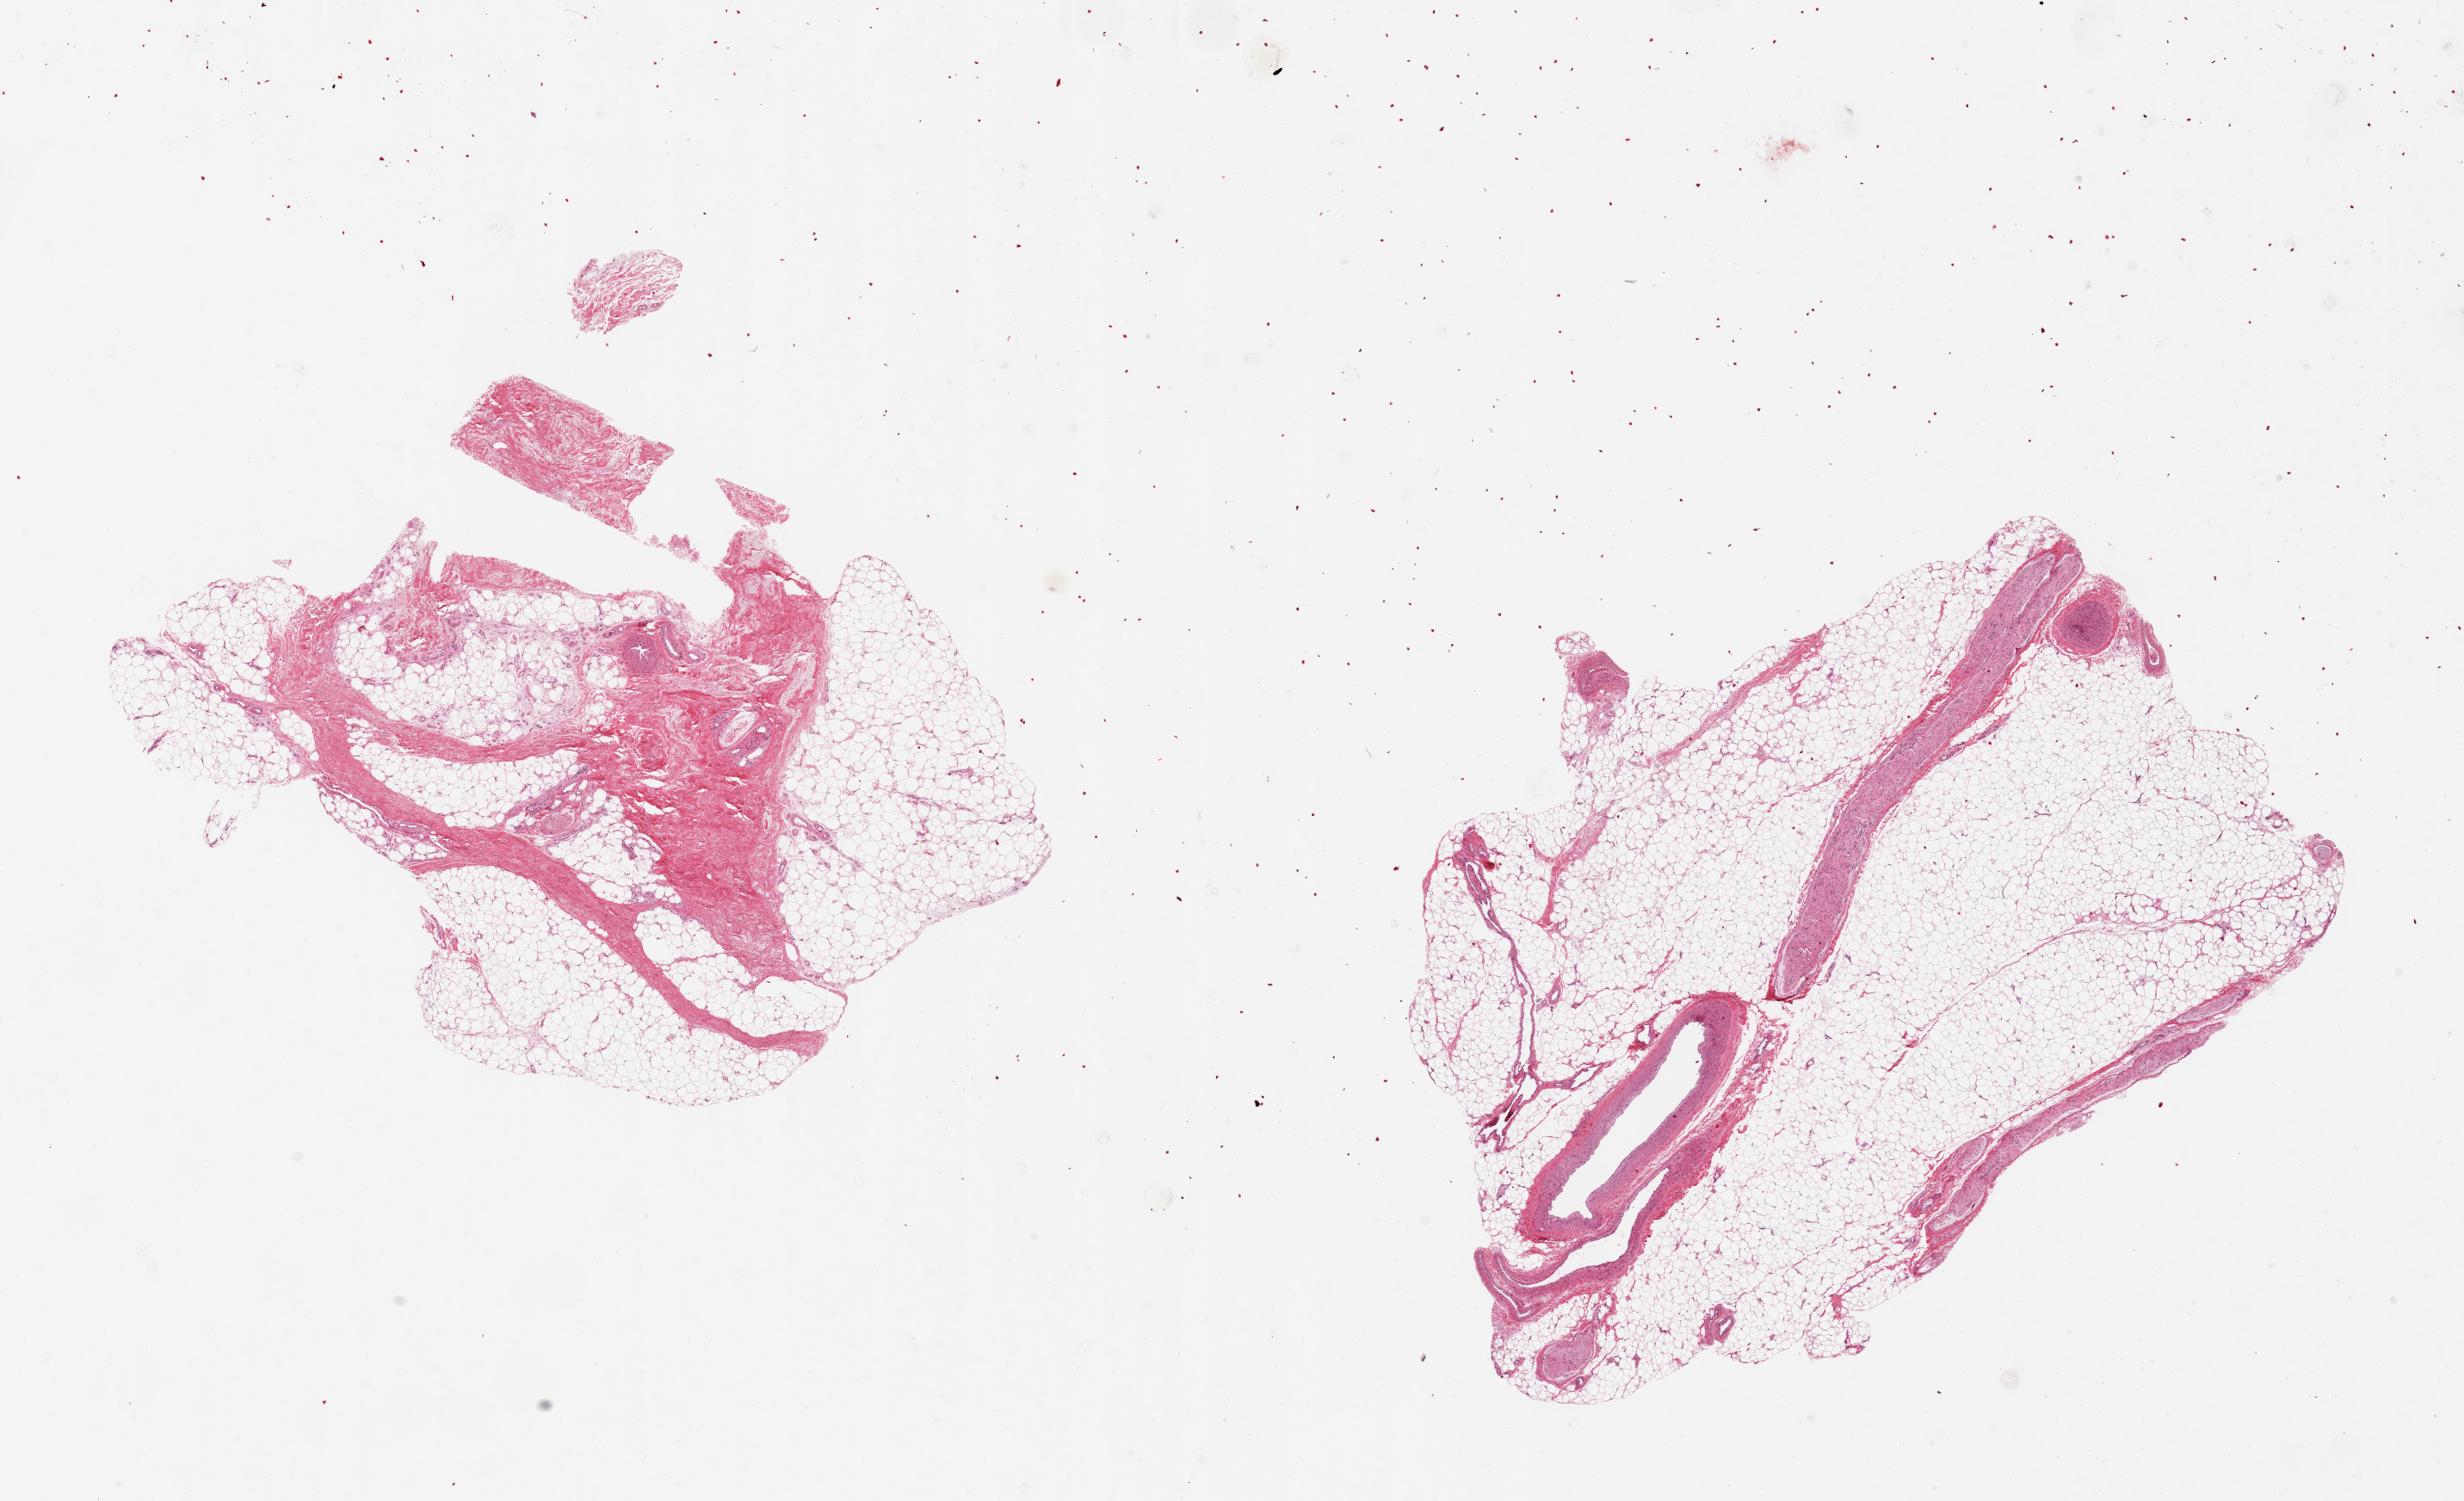
Digitized haematoxylin and eosin-stained section — a low-resolution overview of the entire scanned area, about 22.6 x 13.8 mm (slide scanned at 20x). PAXgene-fixed paraffin-embedded (PFPE) section. Sampled site (target tissue): adipose tissue. Tissue donor sample.
Reviewer comment on this tissue sample: 2 pieces 9x5 & 7x6 mm; ~30% fibrous tissue in 1 and ~10% nerves & artery in other; no artifacts.